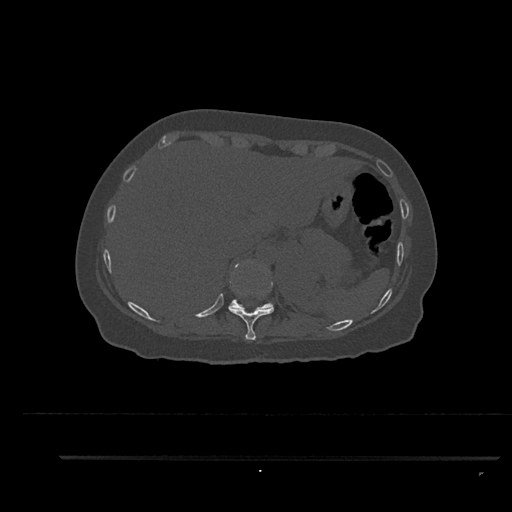
CT including the spine, one axial slice. Position 346 of 797 along the scan axis. 120 kVp. Bone window (W 1800 / L 400 HU). 0.5 mm slice thickness. 512 × 512 image matrix, field of view 408 × 408 mm. Patient: female, 44 years. Case-level facts recorded for this patient, not image findings: primary cancer: renal.
Outlined on this slice (semi-automatically segmented with operator editing):
- T10 vertebra: bounding box [x1, y1, x2, y2] px = [228, 289, 274, 340]
- T11 vertebra: [229, 263, 274, 310]